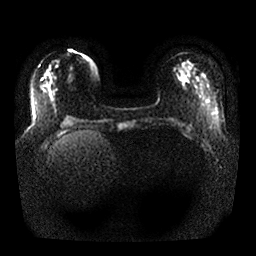
Breast MRI, one axial slice. Slice 8 of 25 in the series (ordered by position). Diffusion-weighted series; image 2 of 4 stored at this slice position (different b-values; order by instance number). 1.5 T. 4 mm slice thickness. 256 × 256 image matrix, field of view 350 × 350 mm. Female patient.
Outlined on this slice (manually delineated by an expert):
- tumour on diffusion-weighted imaging: bounding box (x1, y1, x2, y2) in pixels: (178, 69, 184, 77)